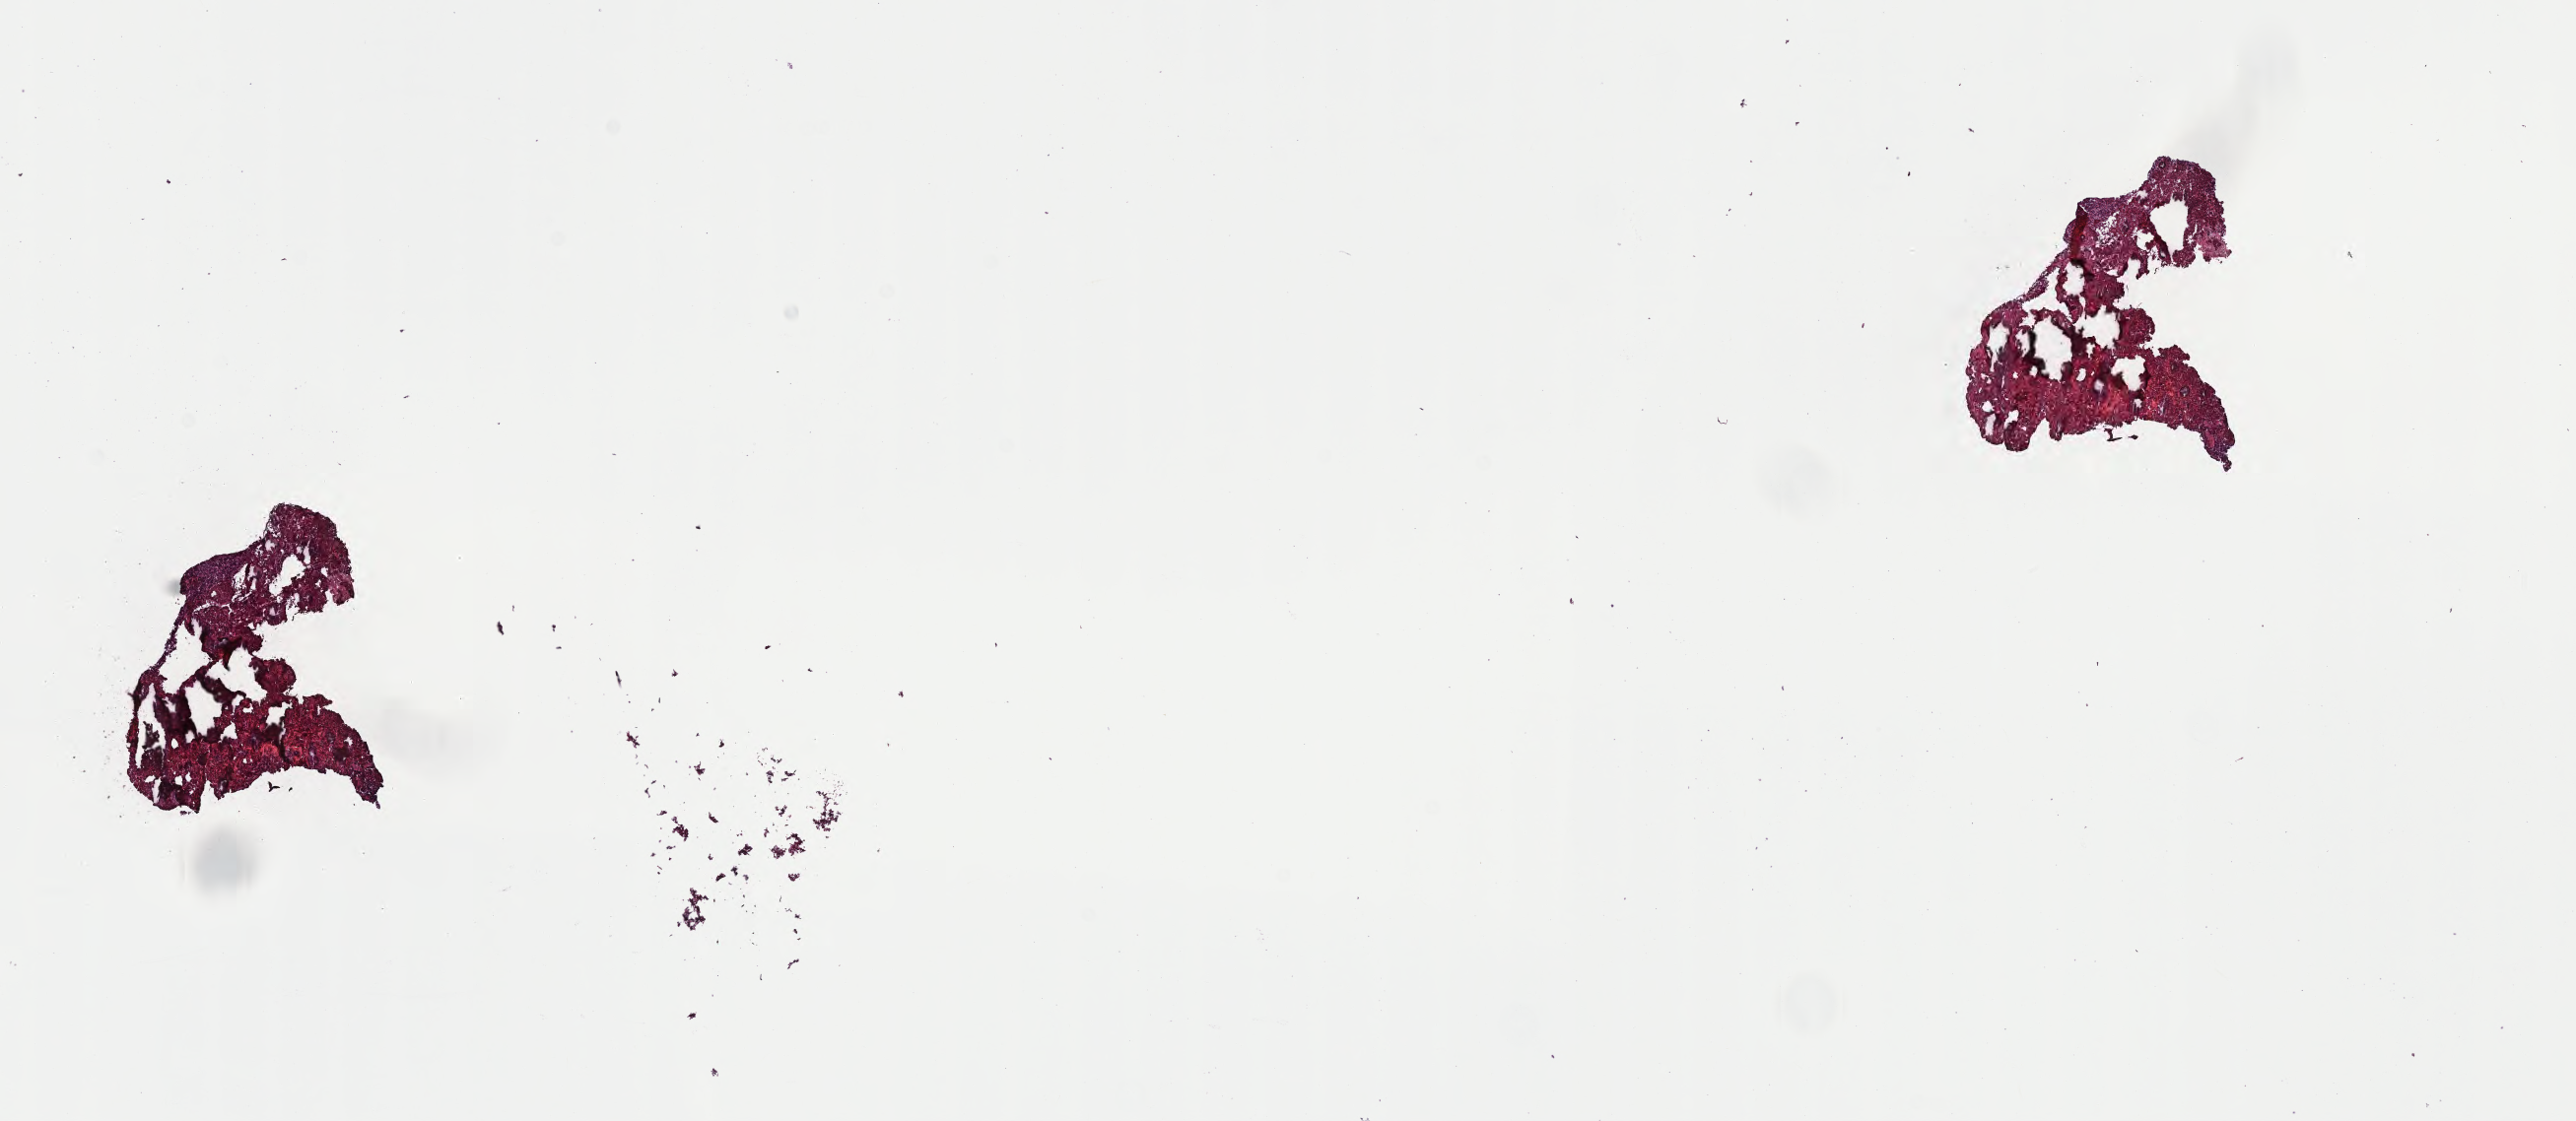
Digitized H&E-stained section of tumor tissue from the brain — a low-resolution overview of the entire scanned area, about 21.1 x 9.2 mm, frozen section (OCT-embedded). Female patient, age 140 months.
• diagnosis (ICD-O-3 morphology term): Pineoblastoma